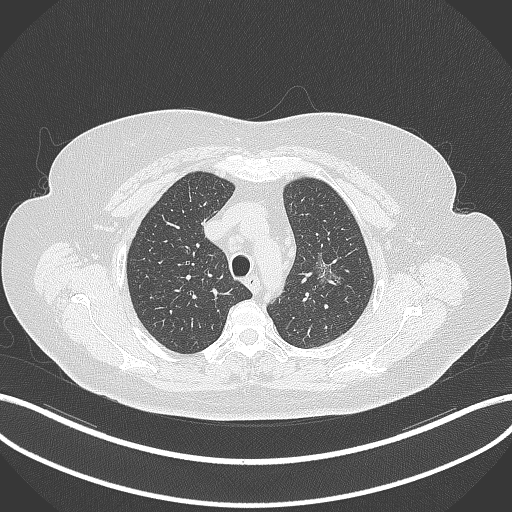
Chest CT, one axial slice. Slice 263 of 309 in the series (ordered by position). Lung window (W 1500 / L -600 HU). 1 mm slice thickness. 512 × 512 image matrix, field of view 400 × 400 mm. Patient: female, 70 years. Case-level facts recorded for this patient, not image findings: clinical TNM (as recorded): T1c N0 M0.
Structures marked on this image (rectangle marked by the reading radiologist):
- lung tumour (recorded histology: adenocarcinoma): bounding box (x1, y1, x2, y2) in pixels: (311, 249, 346, 293)